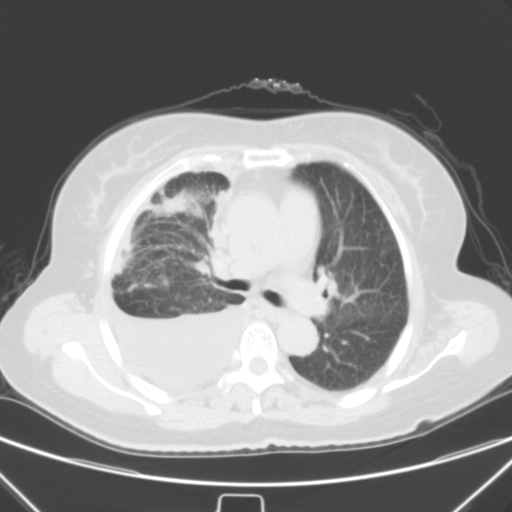
Chest CT, one axial slice. Slice 37 of 55 in the series (ordered by position). 120 kVp. Lung window (W 1500 / L -600 HU). 512 × 512 image matrix, field of view 352 × 352 mm. Female patient, age 66 years. Case-level facts recorded for this patient, not image findings: clinical TNM (as recorded): T2 N0 M1.
Structures marked on this image (bounding box drawn by a radiologist):
- lung tumour (recorded histology: adenocarcinoma): bounding box <157,194,191,217> (left, top, right, bottom; pixels)